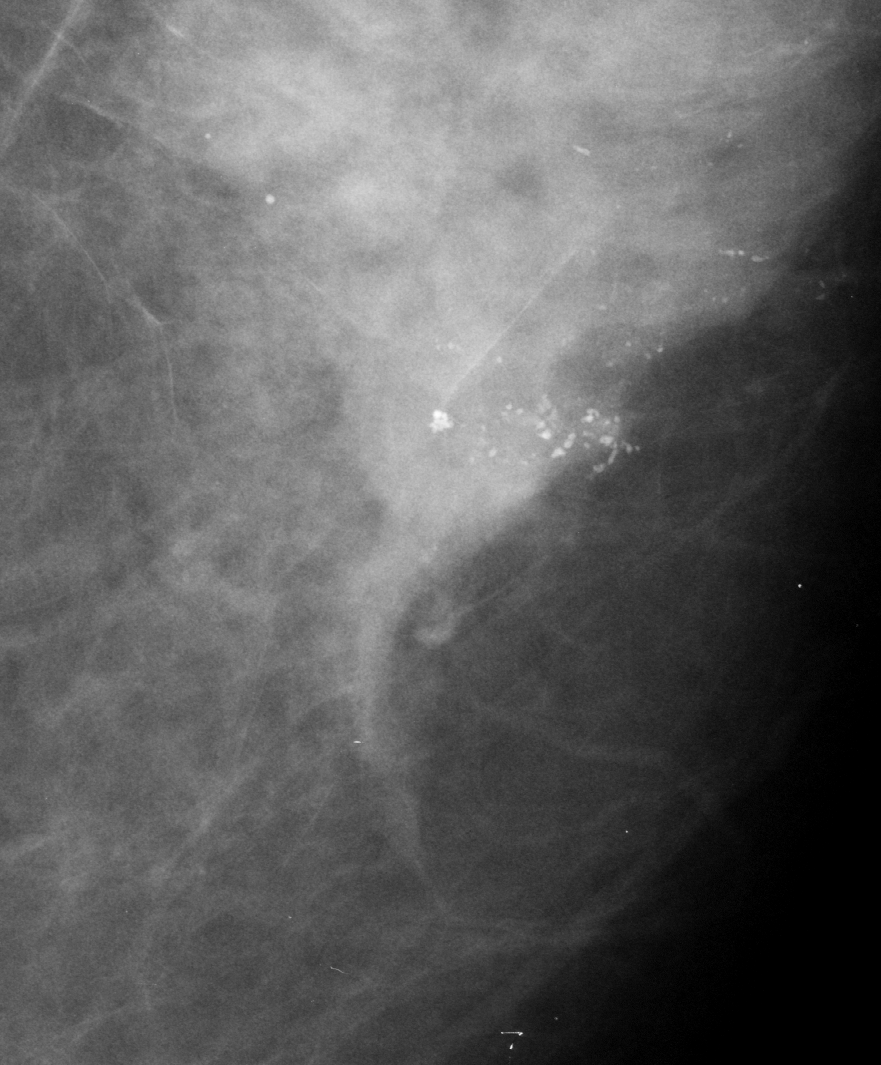
Cropped region of a digitized screen-film mammogram centred on a radiologist-marked abnormality, left breast, CC view, BI-RADS breast density category 3 (scale 1–4).
Calcifications, morphology pleomorphic, distribution segmental; BI-RADS assessment category 5; pathology (as recorded): malignant.